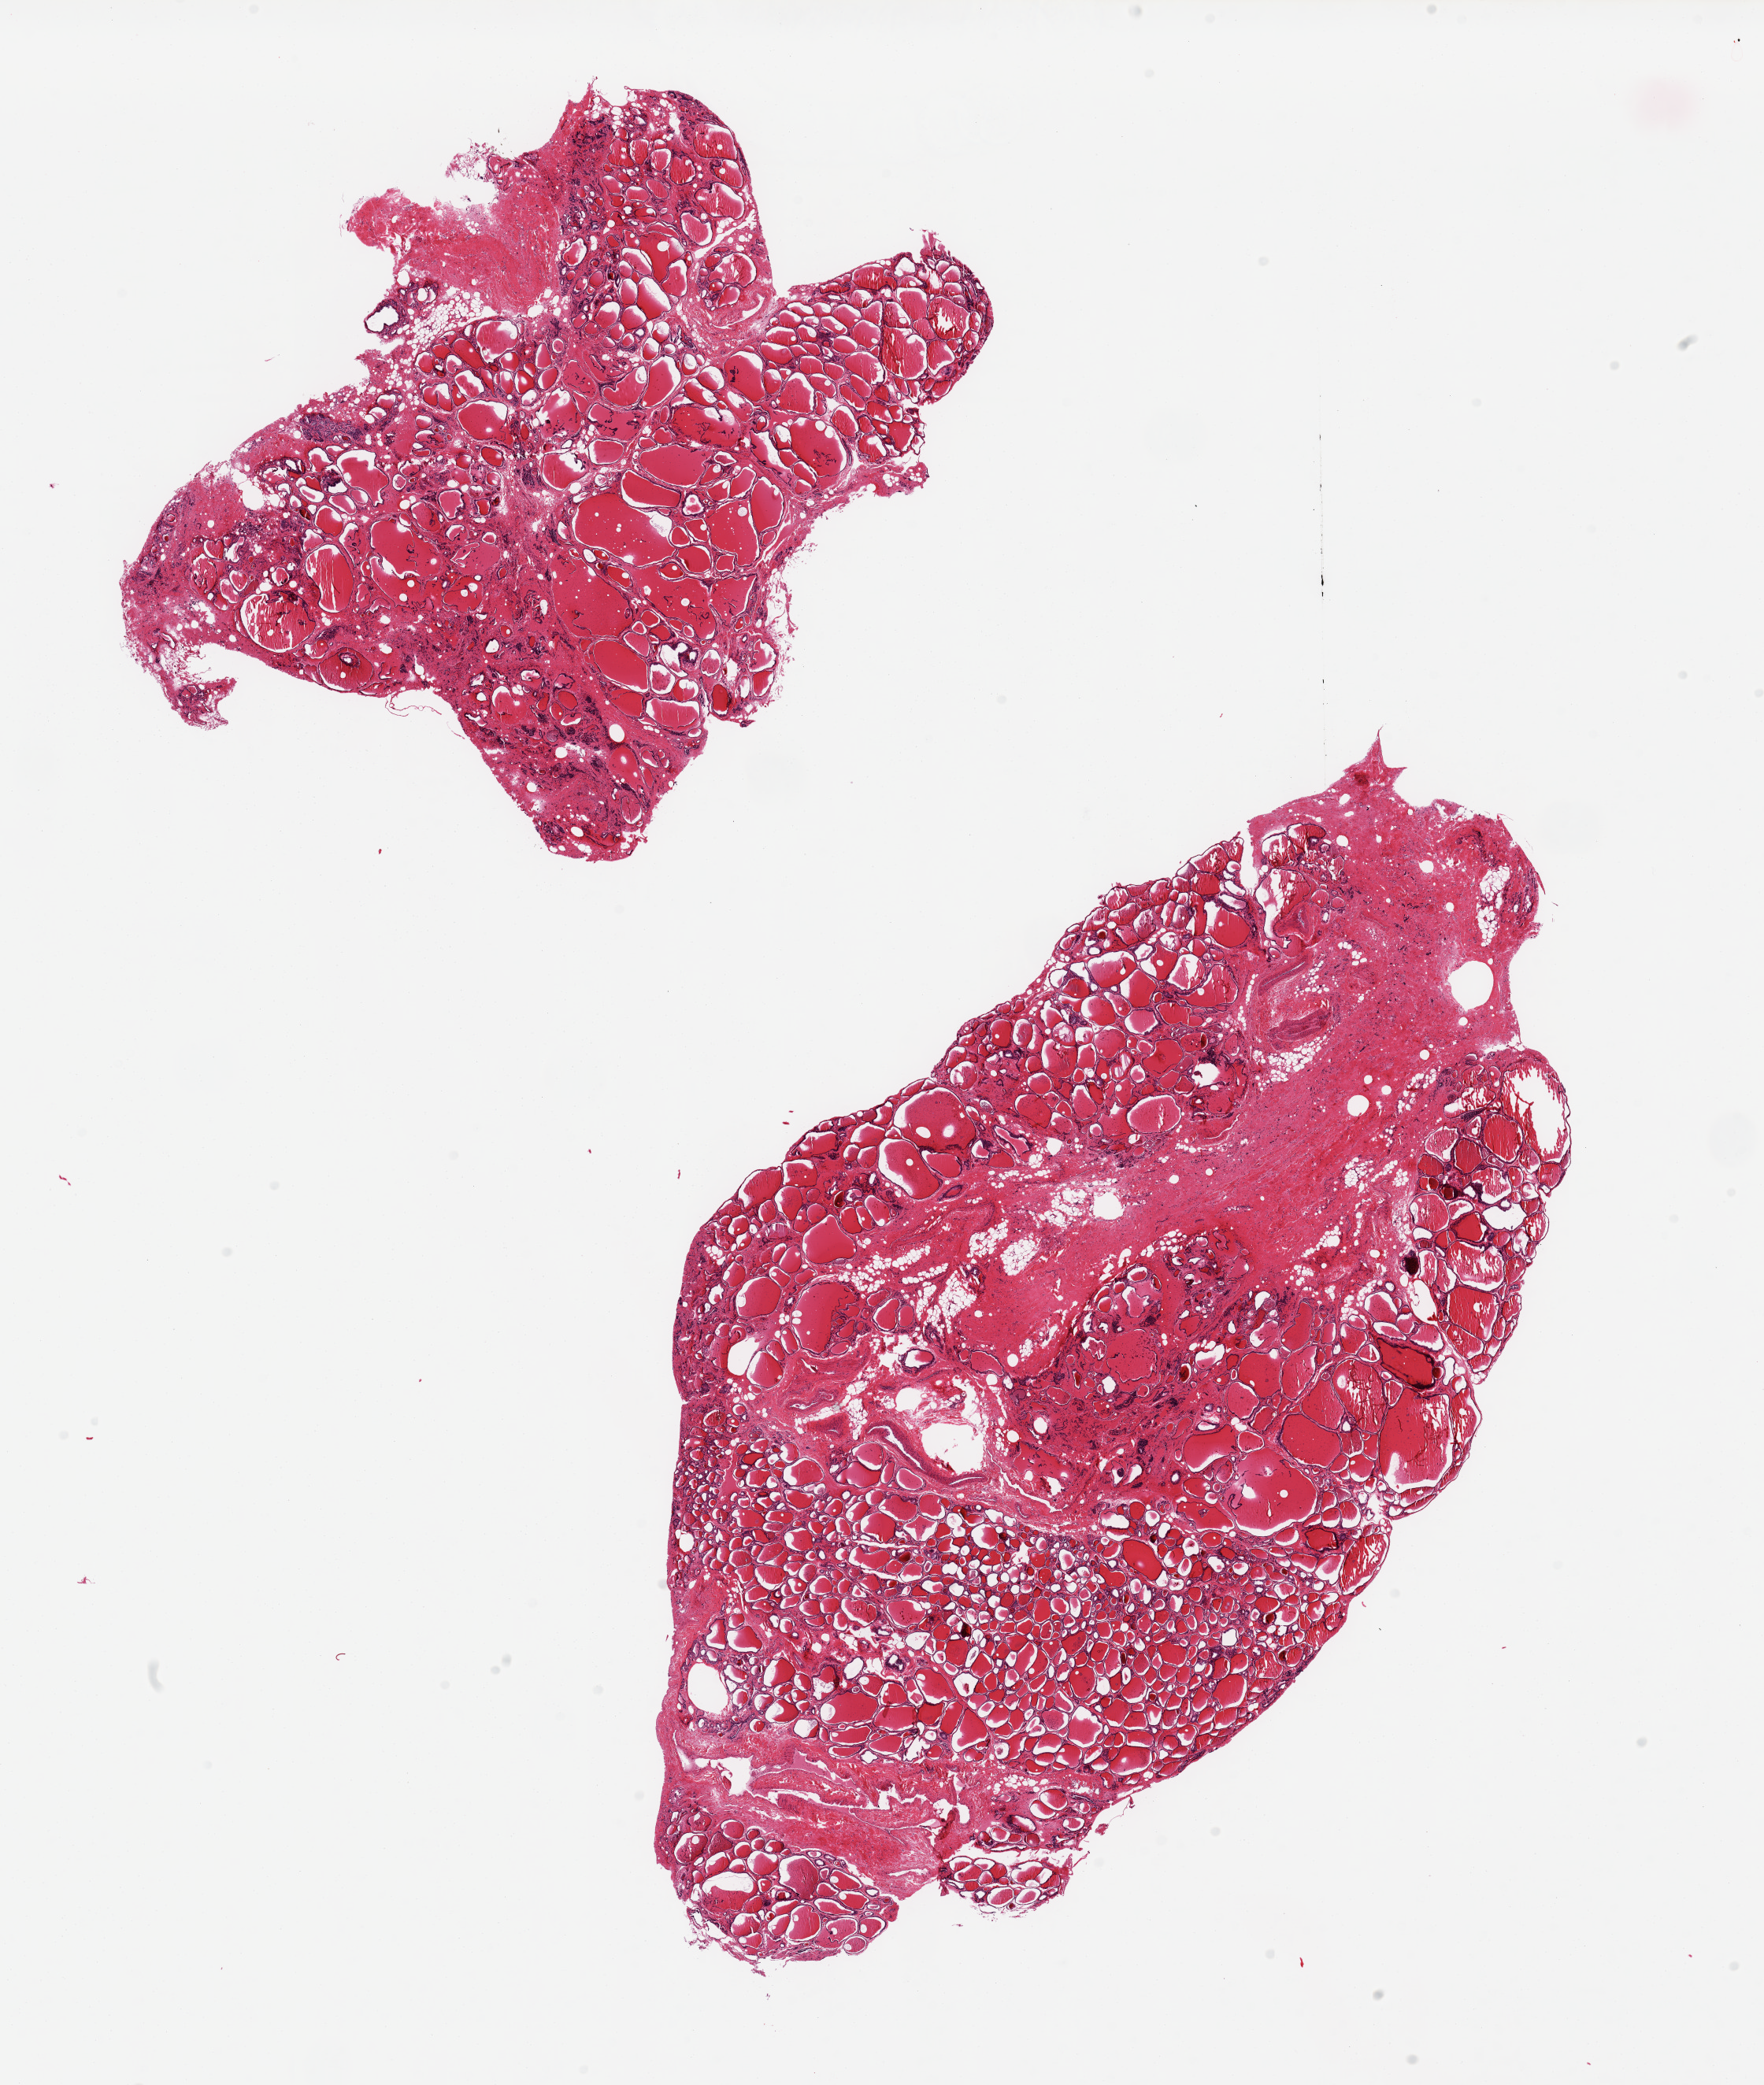
Haematoxylin and eosin whole-slide image, low-resolution overview of the scanned area, about 17.7 x 20.9 mm; PAXgene-fixed, paraffin-embedded tissue; target tissue: thyroid; donor tissue sample. Donor sex: male.
• reviewer comment on this tissue sample: 2 pieces, nodular goitre; regressive changes